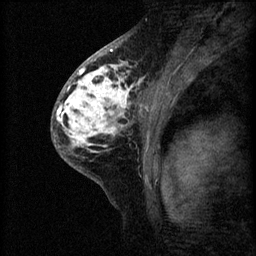
Breast MRI (dynamic contrast-enhanced), one sagittal slice; slice 37 of 60 in the series (ordered by position); 3 images stored at this slice position (order not interpretable as contrast timing); 1.5 T; TE 4.2 ms, TR 8.2 ms; 256 × 256 image matrix. Female patient, age 41 years.
Outlined on this slice (semi-automatically segmented with operator editing):
- analysis volume of interest (the breast-tissue region the enhancement analysis was run in; not a lesion): bounding box (x1, y1, x2, y2) in pixels: (53, 62, 160, 175)
- tumour enhancement mask (voxels above the 70 % enhancement threshold inside the analysis volume of interest): (56, 64, 147, 153)